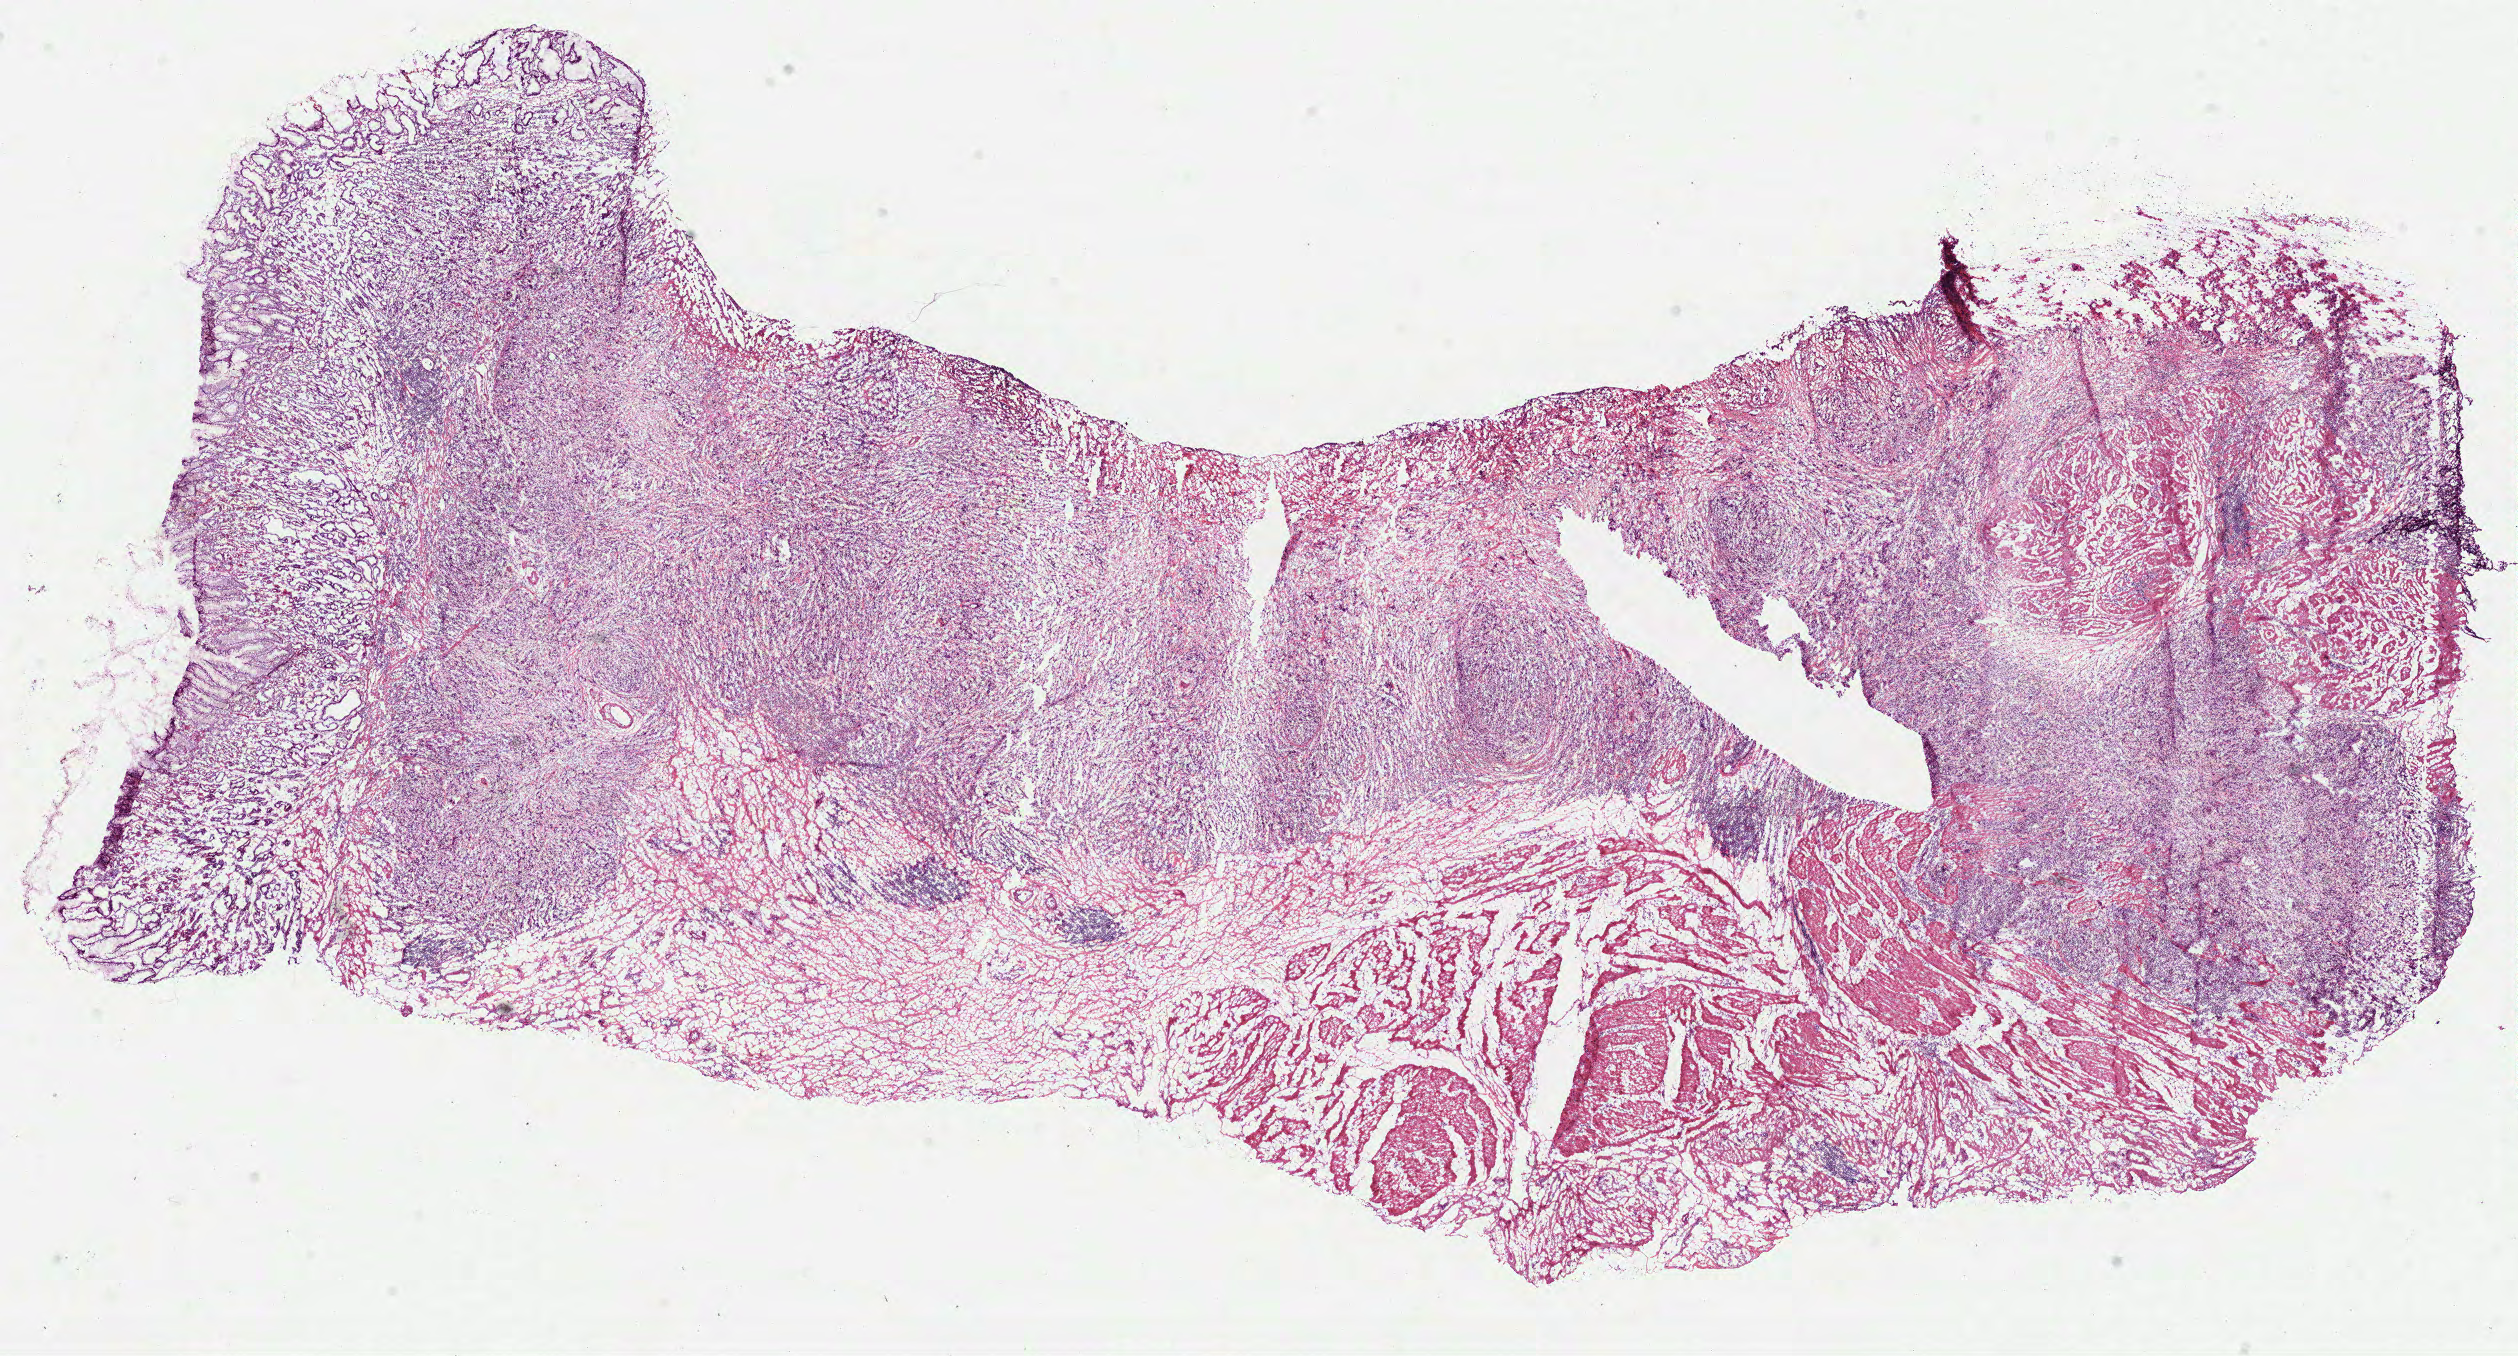
H&E whole-slide image — shown as a low-resolution overview of the whole scanned area (about 20.3 x 10.9 mm), frozen section from the bottom of the tissue portion, stomach, primary tumour sample. Patient: female, age at initial diagnosis 55 years. Histologic grade: G3 (poorly differentiated). Composition of this section per pathologist review: tumour cells 60%, tumour nuclei 70%, normal cells 10%, stromal cells 30%, necrosis 0%.
Diagnosis: Adenocarcinoma, NOS. AJCC pathologic stage: IIB. Lymph nodes positive (case pathology): 0 of 6 examined.